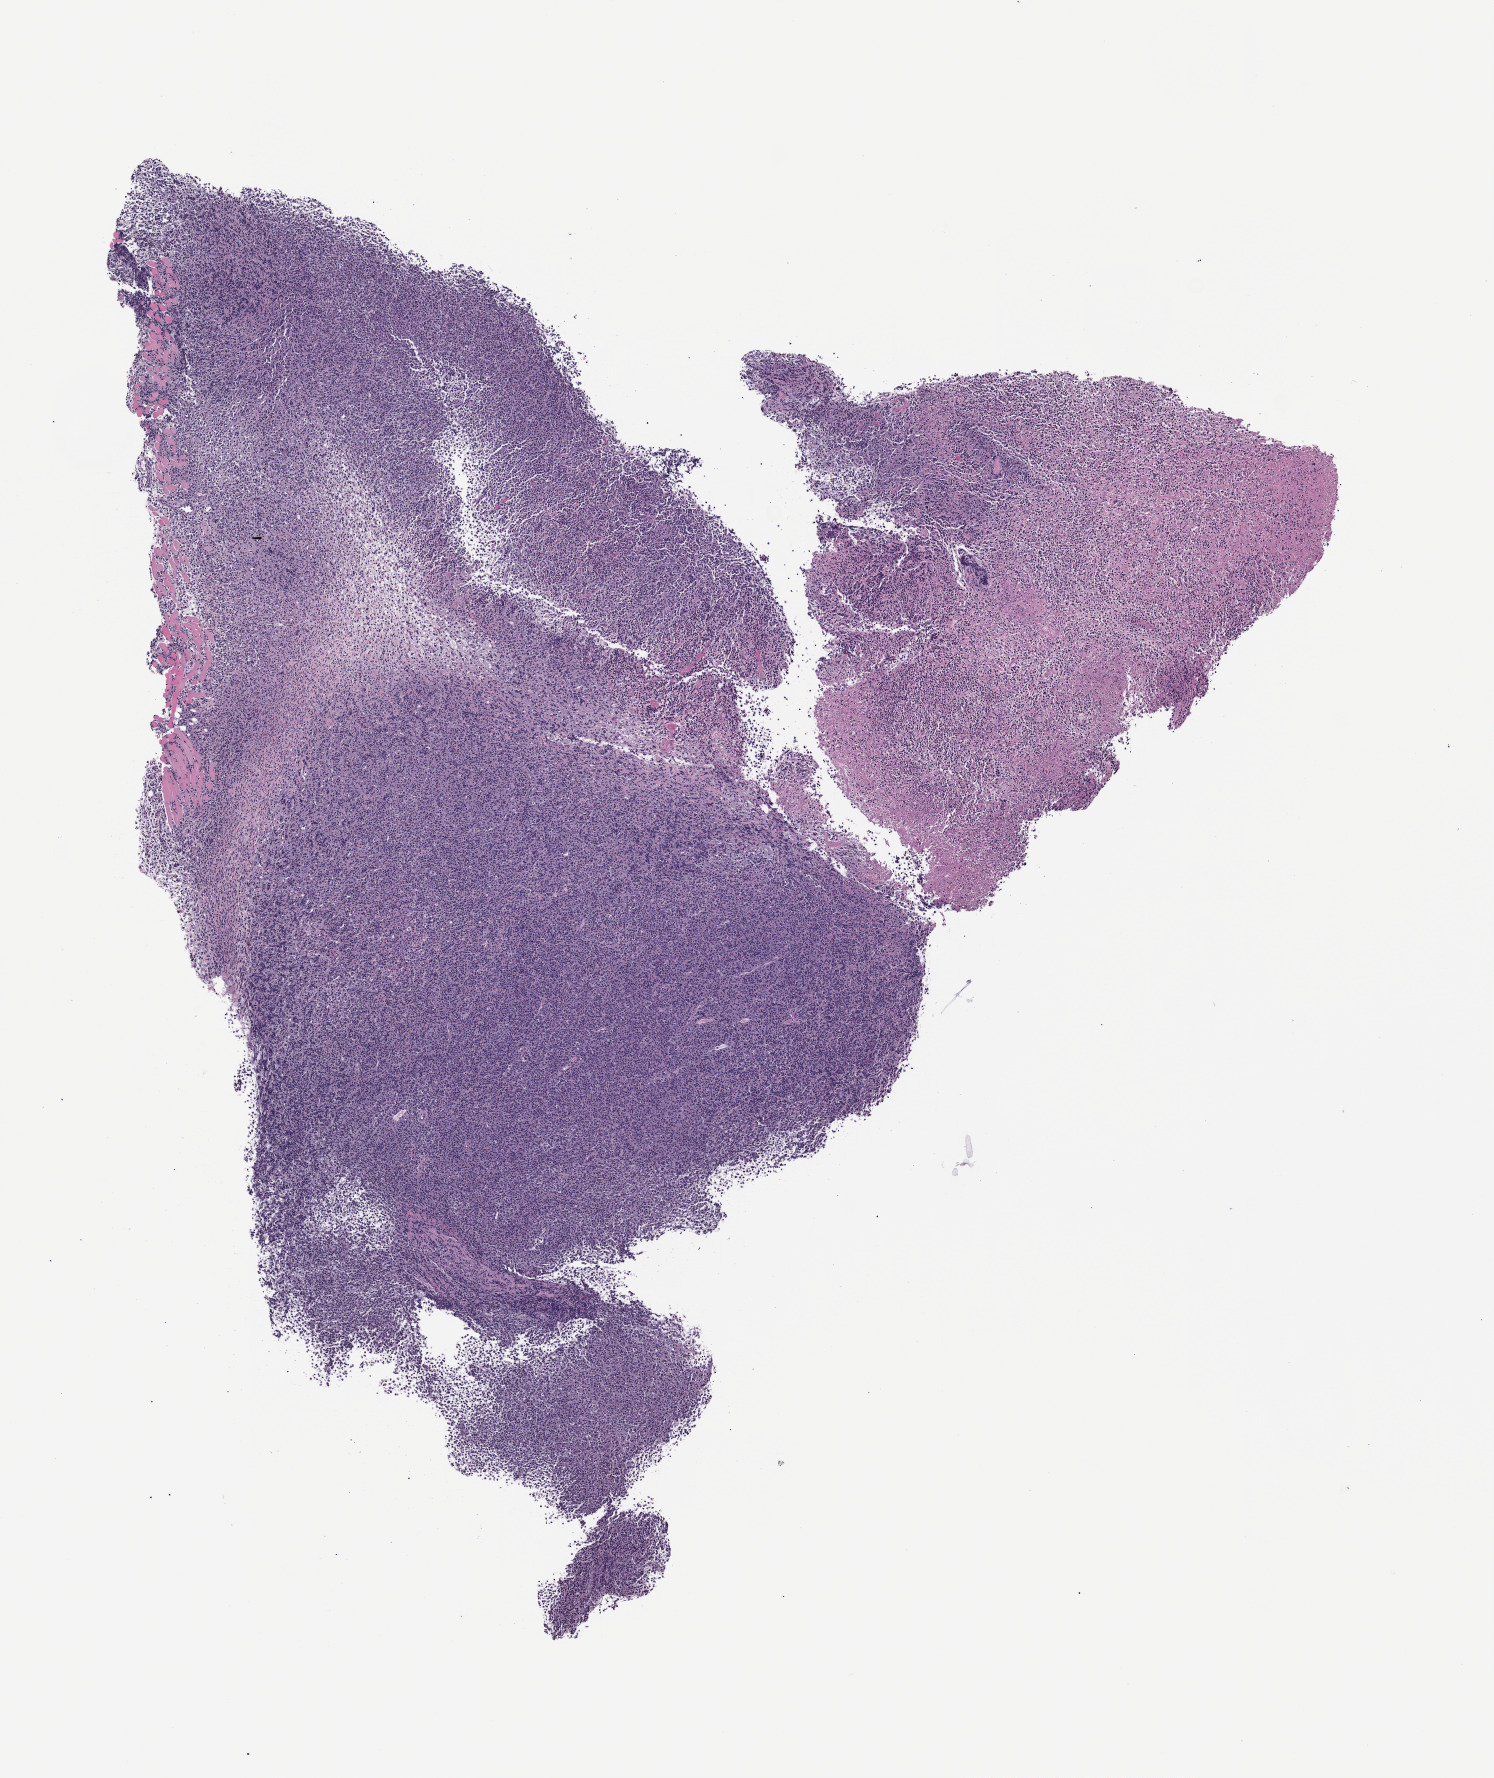
Hematoxylin and eosin (H&E) whole-slide image of a patient-derived xenograft (PDX) tumor grown in a mouse — shown as a low-resolution overview of the whole scanned area (about 6.0 x 7.2 mm).
* specimen: formalin-fixed, paraffin-embedded (FFPE) tissue